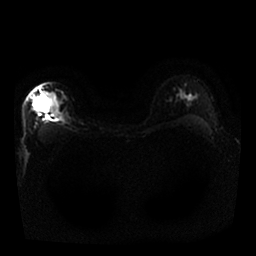
Breast MRI, one axial slice; slice 18 of 25 in the series (ordered by position); diffusion-weighted series; image 2 of 4 stored at this slice position (different b-values; order by instance number); 1.5 T; 256 × 256 image matrix, field of view 340 × 340 mm. Female patient.
Structures marked on this image (manually delineated by an expert):
- tumour on diffusion-weighted imaging: box from (x=35, y=102) to (x=40, y=109) px